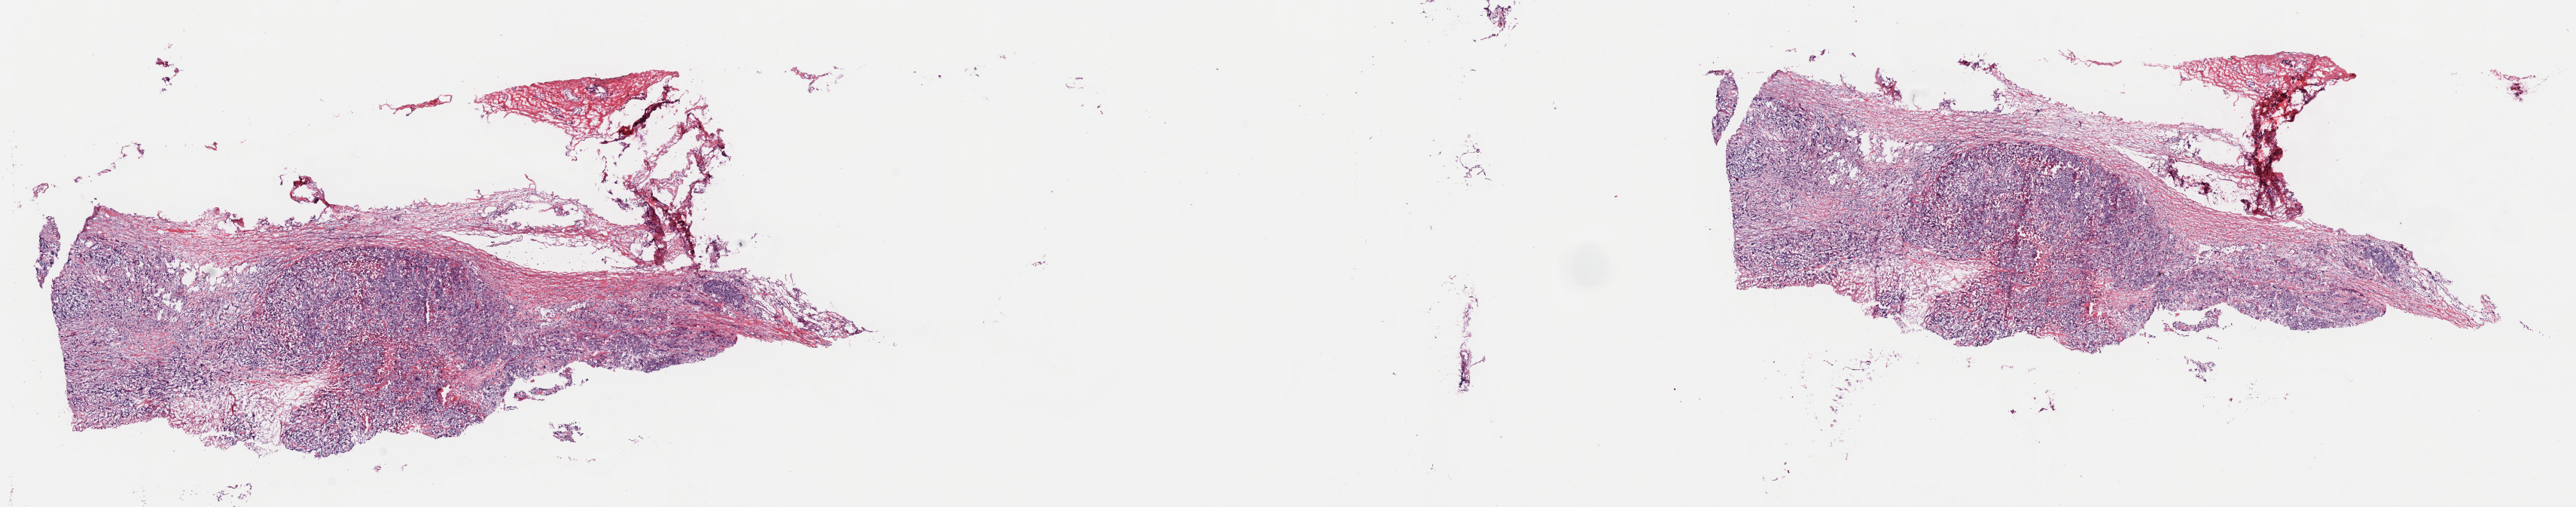
Digitized Hematoxylin and eosin (H&E) stained tissue section (whole slide) — shown as a low-resolution overview of the whole scanned area (about 27.0 x 5.3 mm, slide scanned at 40x). Frozen section from the top of the tissue portion. Sample: primary tumour, bladder. Patient: male, age at initial diagnosis 63 years. Composition of this section per pathologist review: tumour cells 60%, tumour nuclei 70%.
Diagnosis: Transitional cell carcinoma (trigone of bladder).